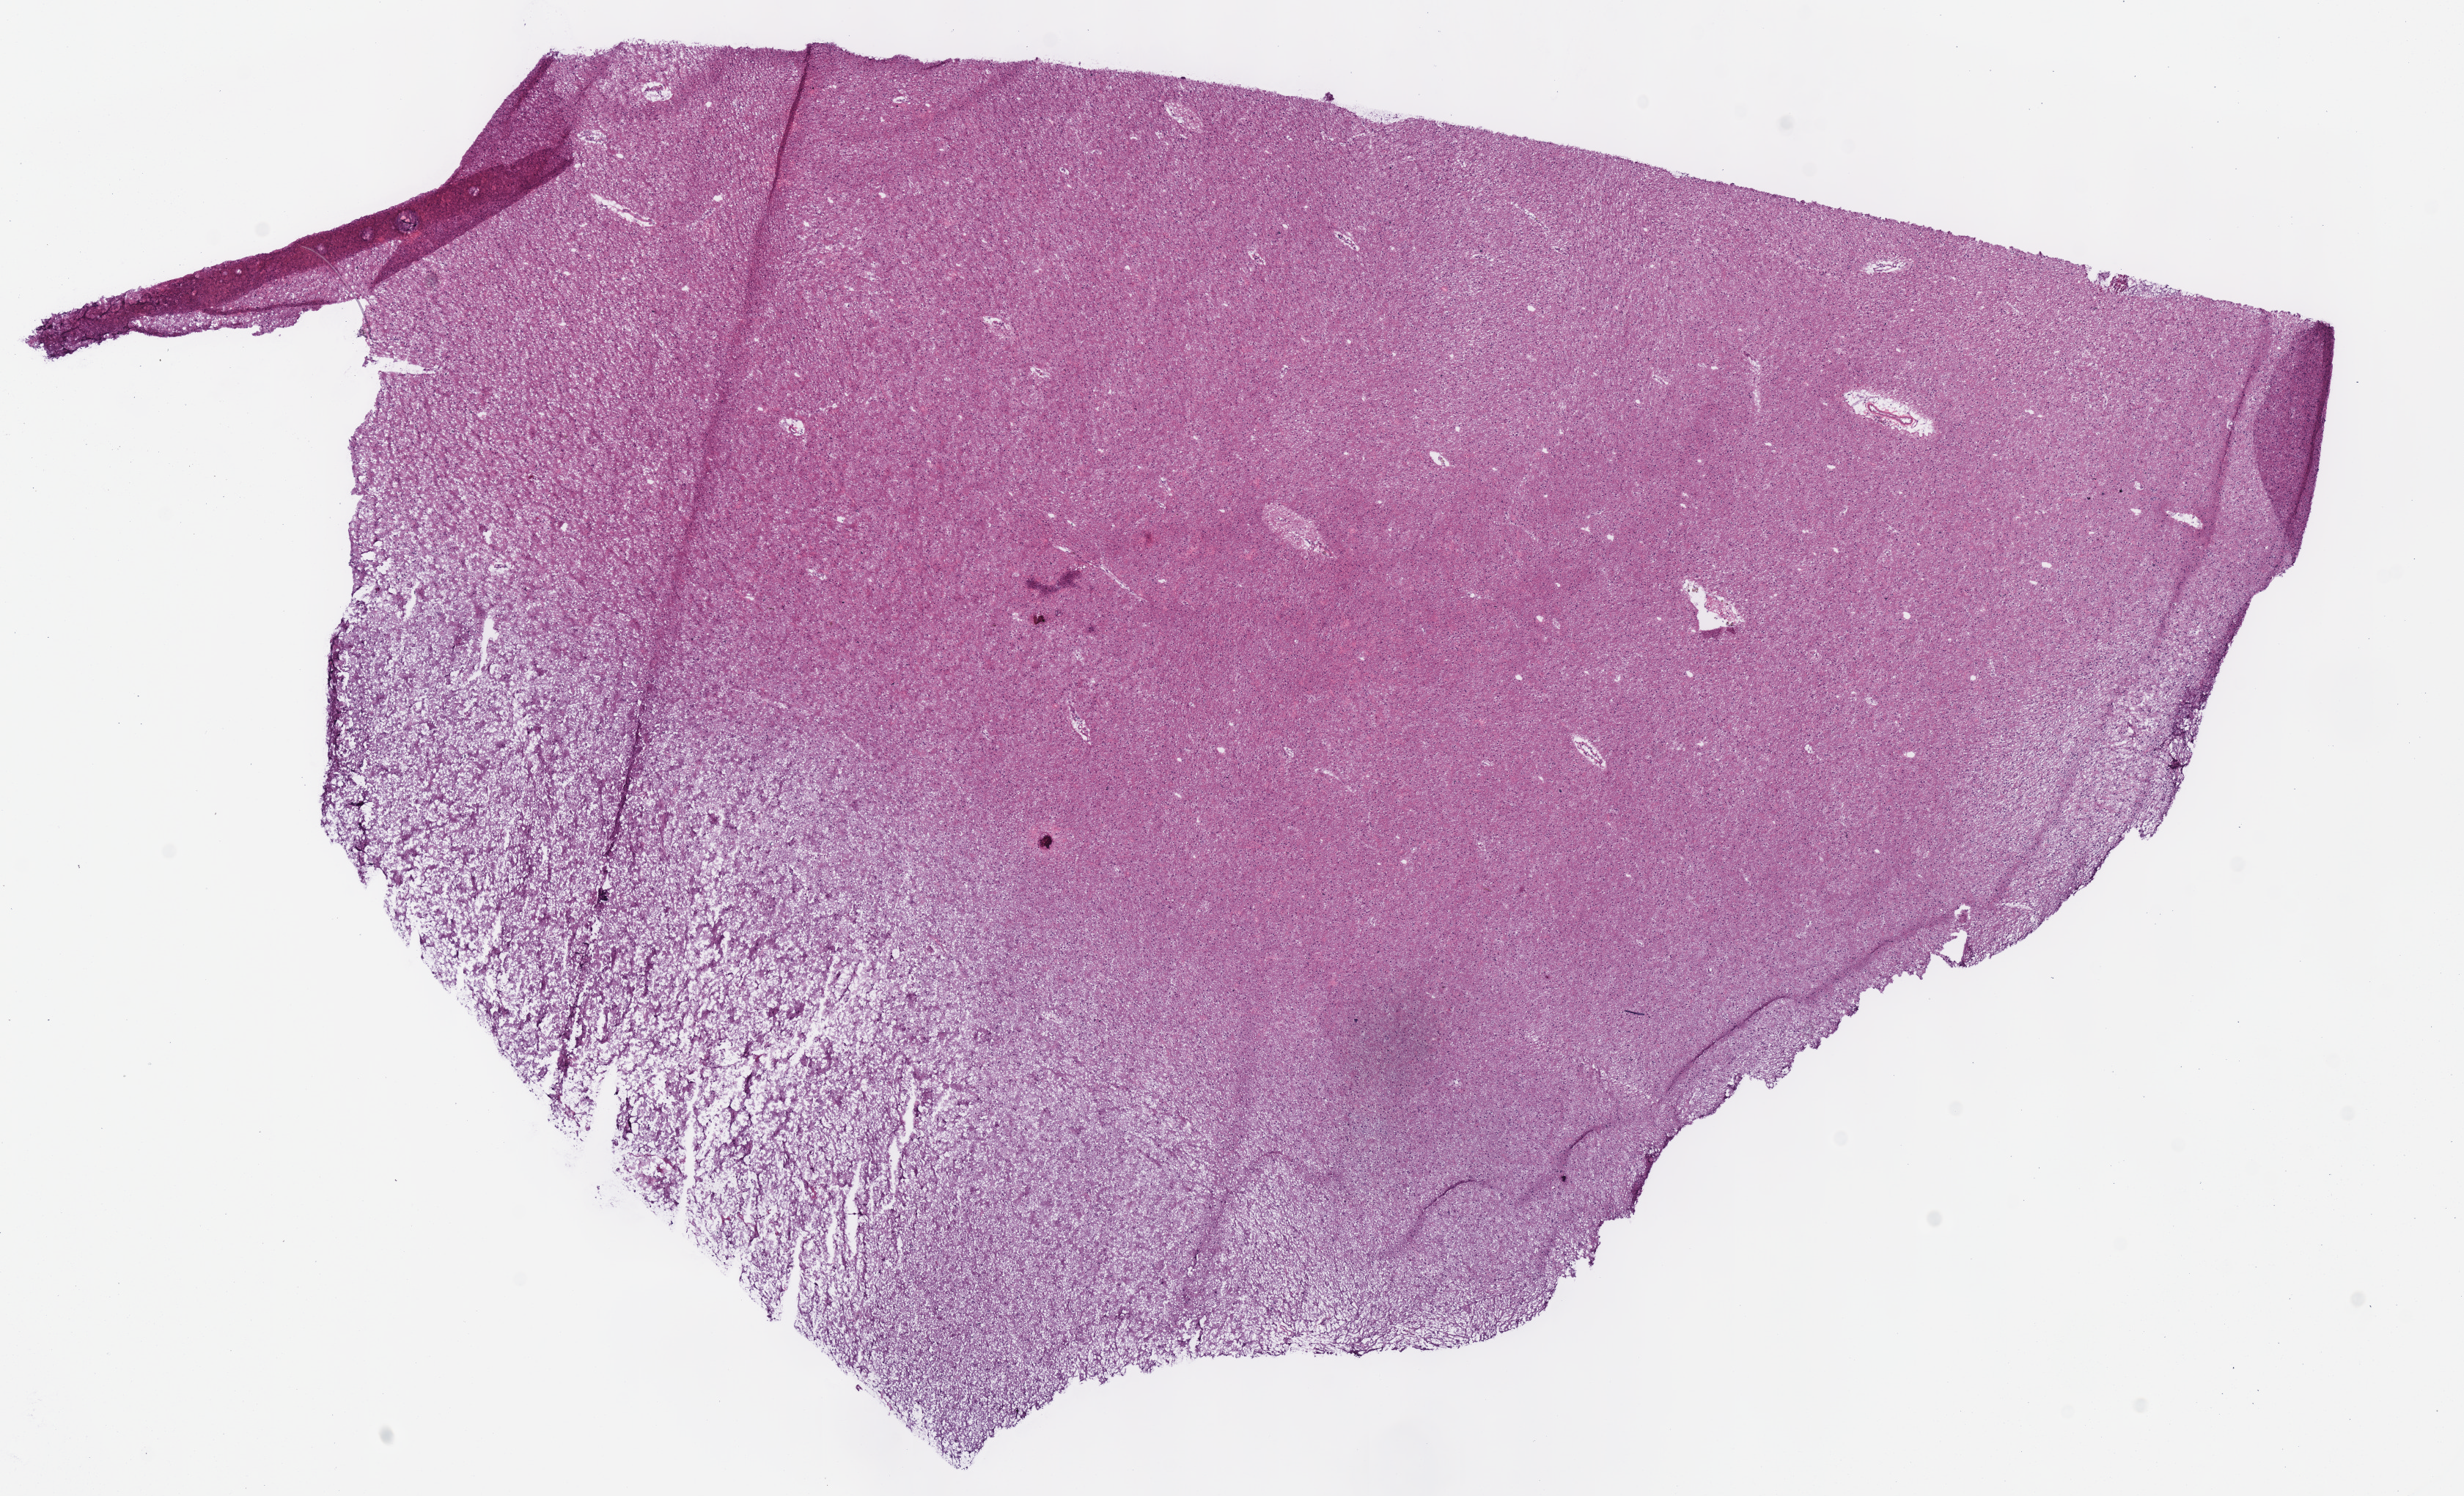
Hematoxylin and eosin (H&E) stained whole-slide image — low-resolution overview of the scanned area, about 13.2 x 8.0 mm. Frozen section from the top of the tissue portion. Sample: primary tumour, brain. Male, age 31 years at initial diagnosis.
Histologic diagnosis: Mixed glioma (cerebrum).